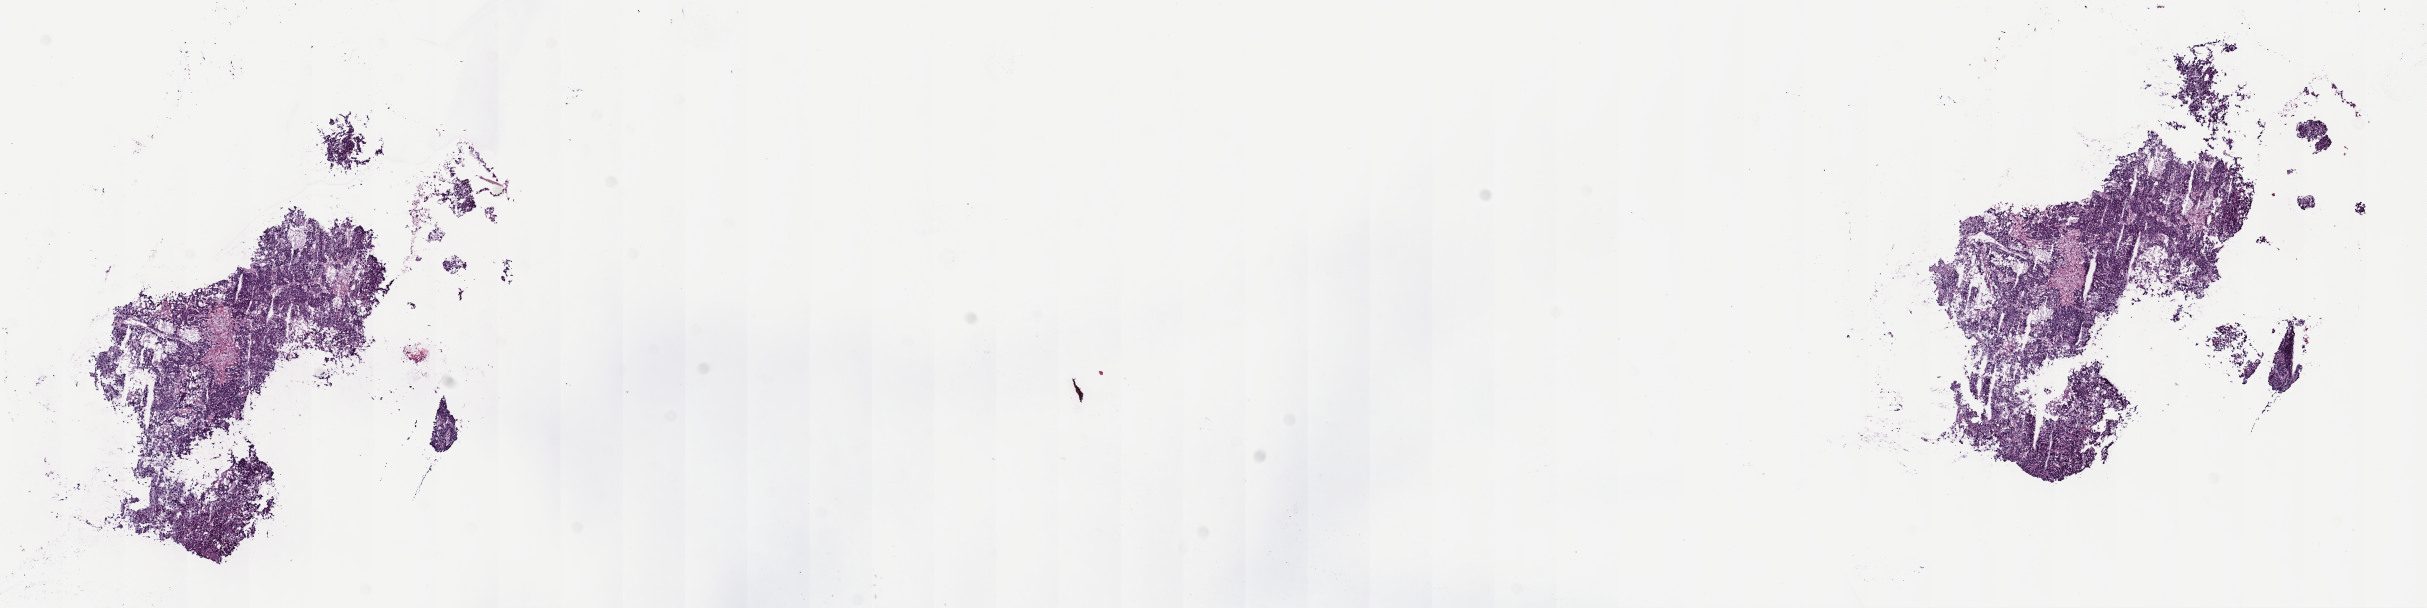
Whole-slide histology image, H&E, whole scanned area (about 19.6 x 4.9 mm, from a 40x scan) shown as a low-resolution overview. Frozen section from the top of the tissue portion. Liver, primary tumour sample. Female, age 73 years at initial diagnosis. Histologic grade: G2 (moderately differentiated). Composition of this section per pathologist review: tumour cells 83%, tumour nuclei 94%, normal cells 0%, stromal cells 9%, necrosis 8%. Infiltration values recorded for this section: lymphocyte infiltration 3%, monocyte infiltration 1%, neutrophil infiltration 1%.
AJCC pathologic stage: I. Histologic diagnosis: Hepatocellular carcinoma, NOS.